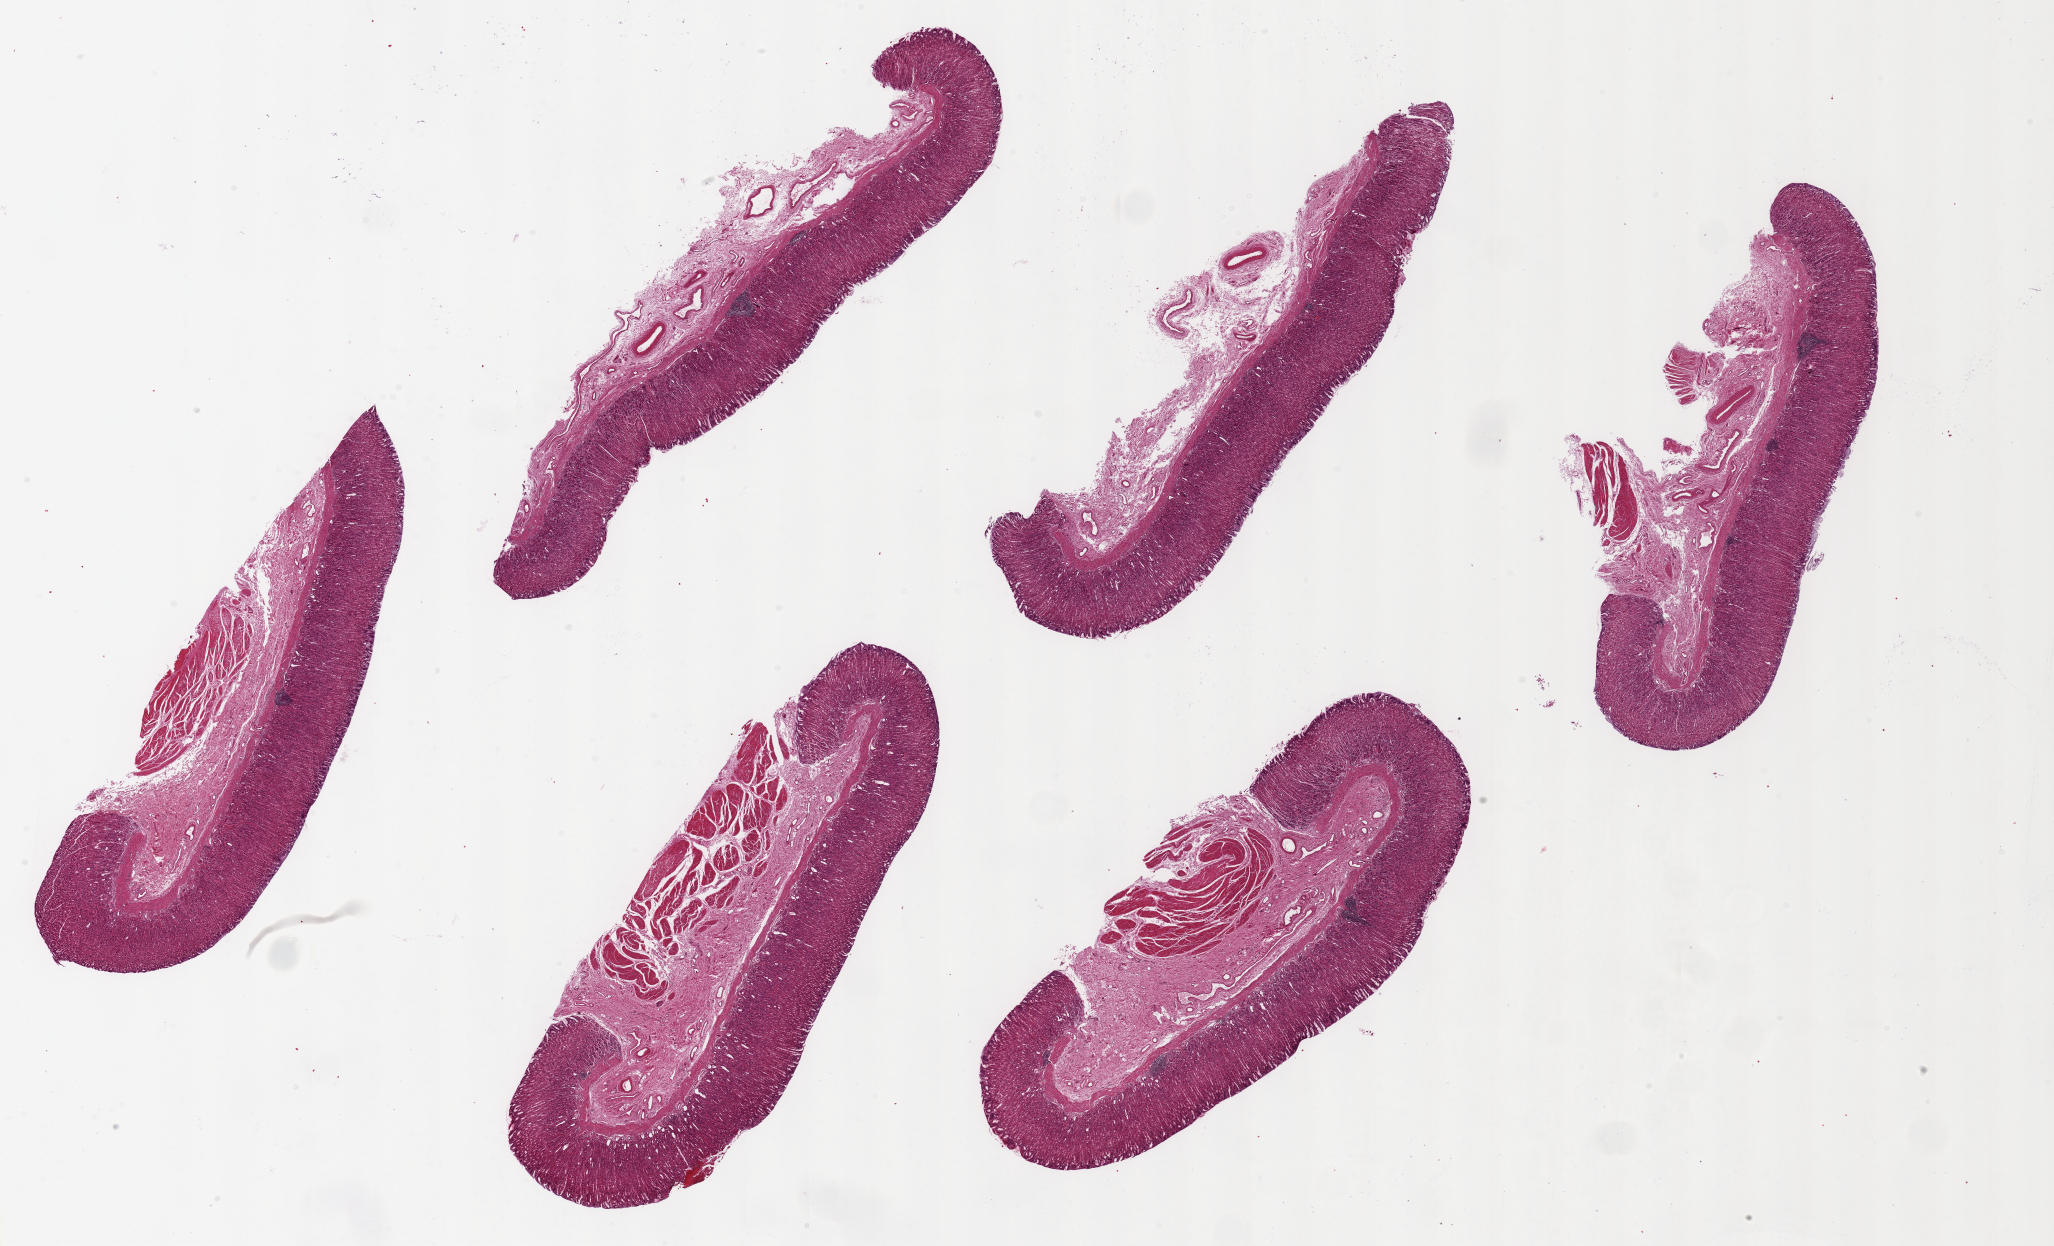
Digitized H&E-stained section, low-resolution overview of the scanned area, about 32.5 x 19.7 mm (slide scanned at 20x), PAXgene-fixed, paraffin-embedded tissue, section of stomach (target tissue), donor tissue sample. Donor sex: male.
Pathologist's review note for this sample: 6 pieces,~10x2.5mm; Mucosa extremely well preserved, 30-50% of thickness; Basal lymphoid aggregates.